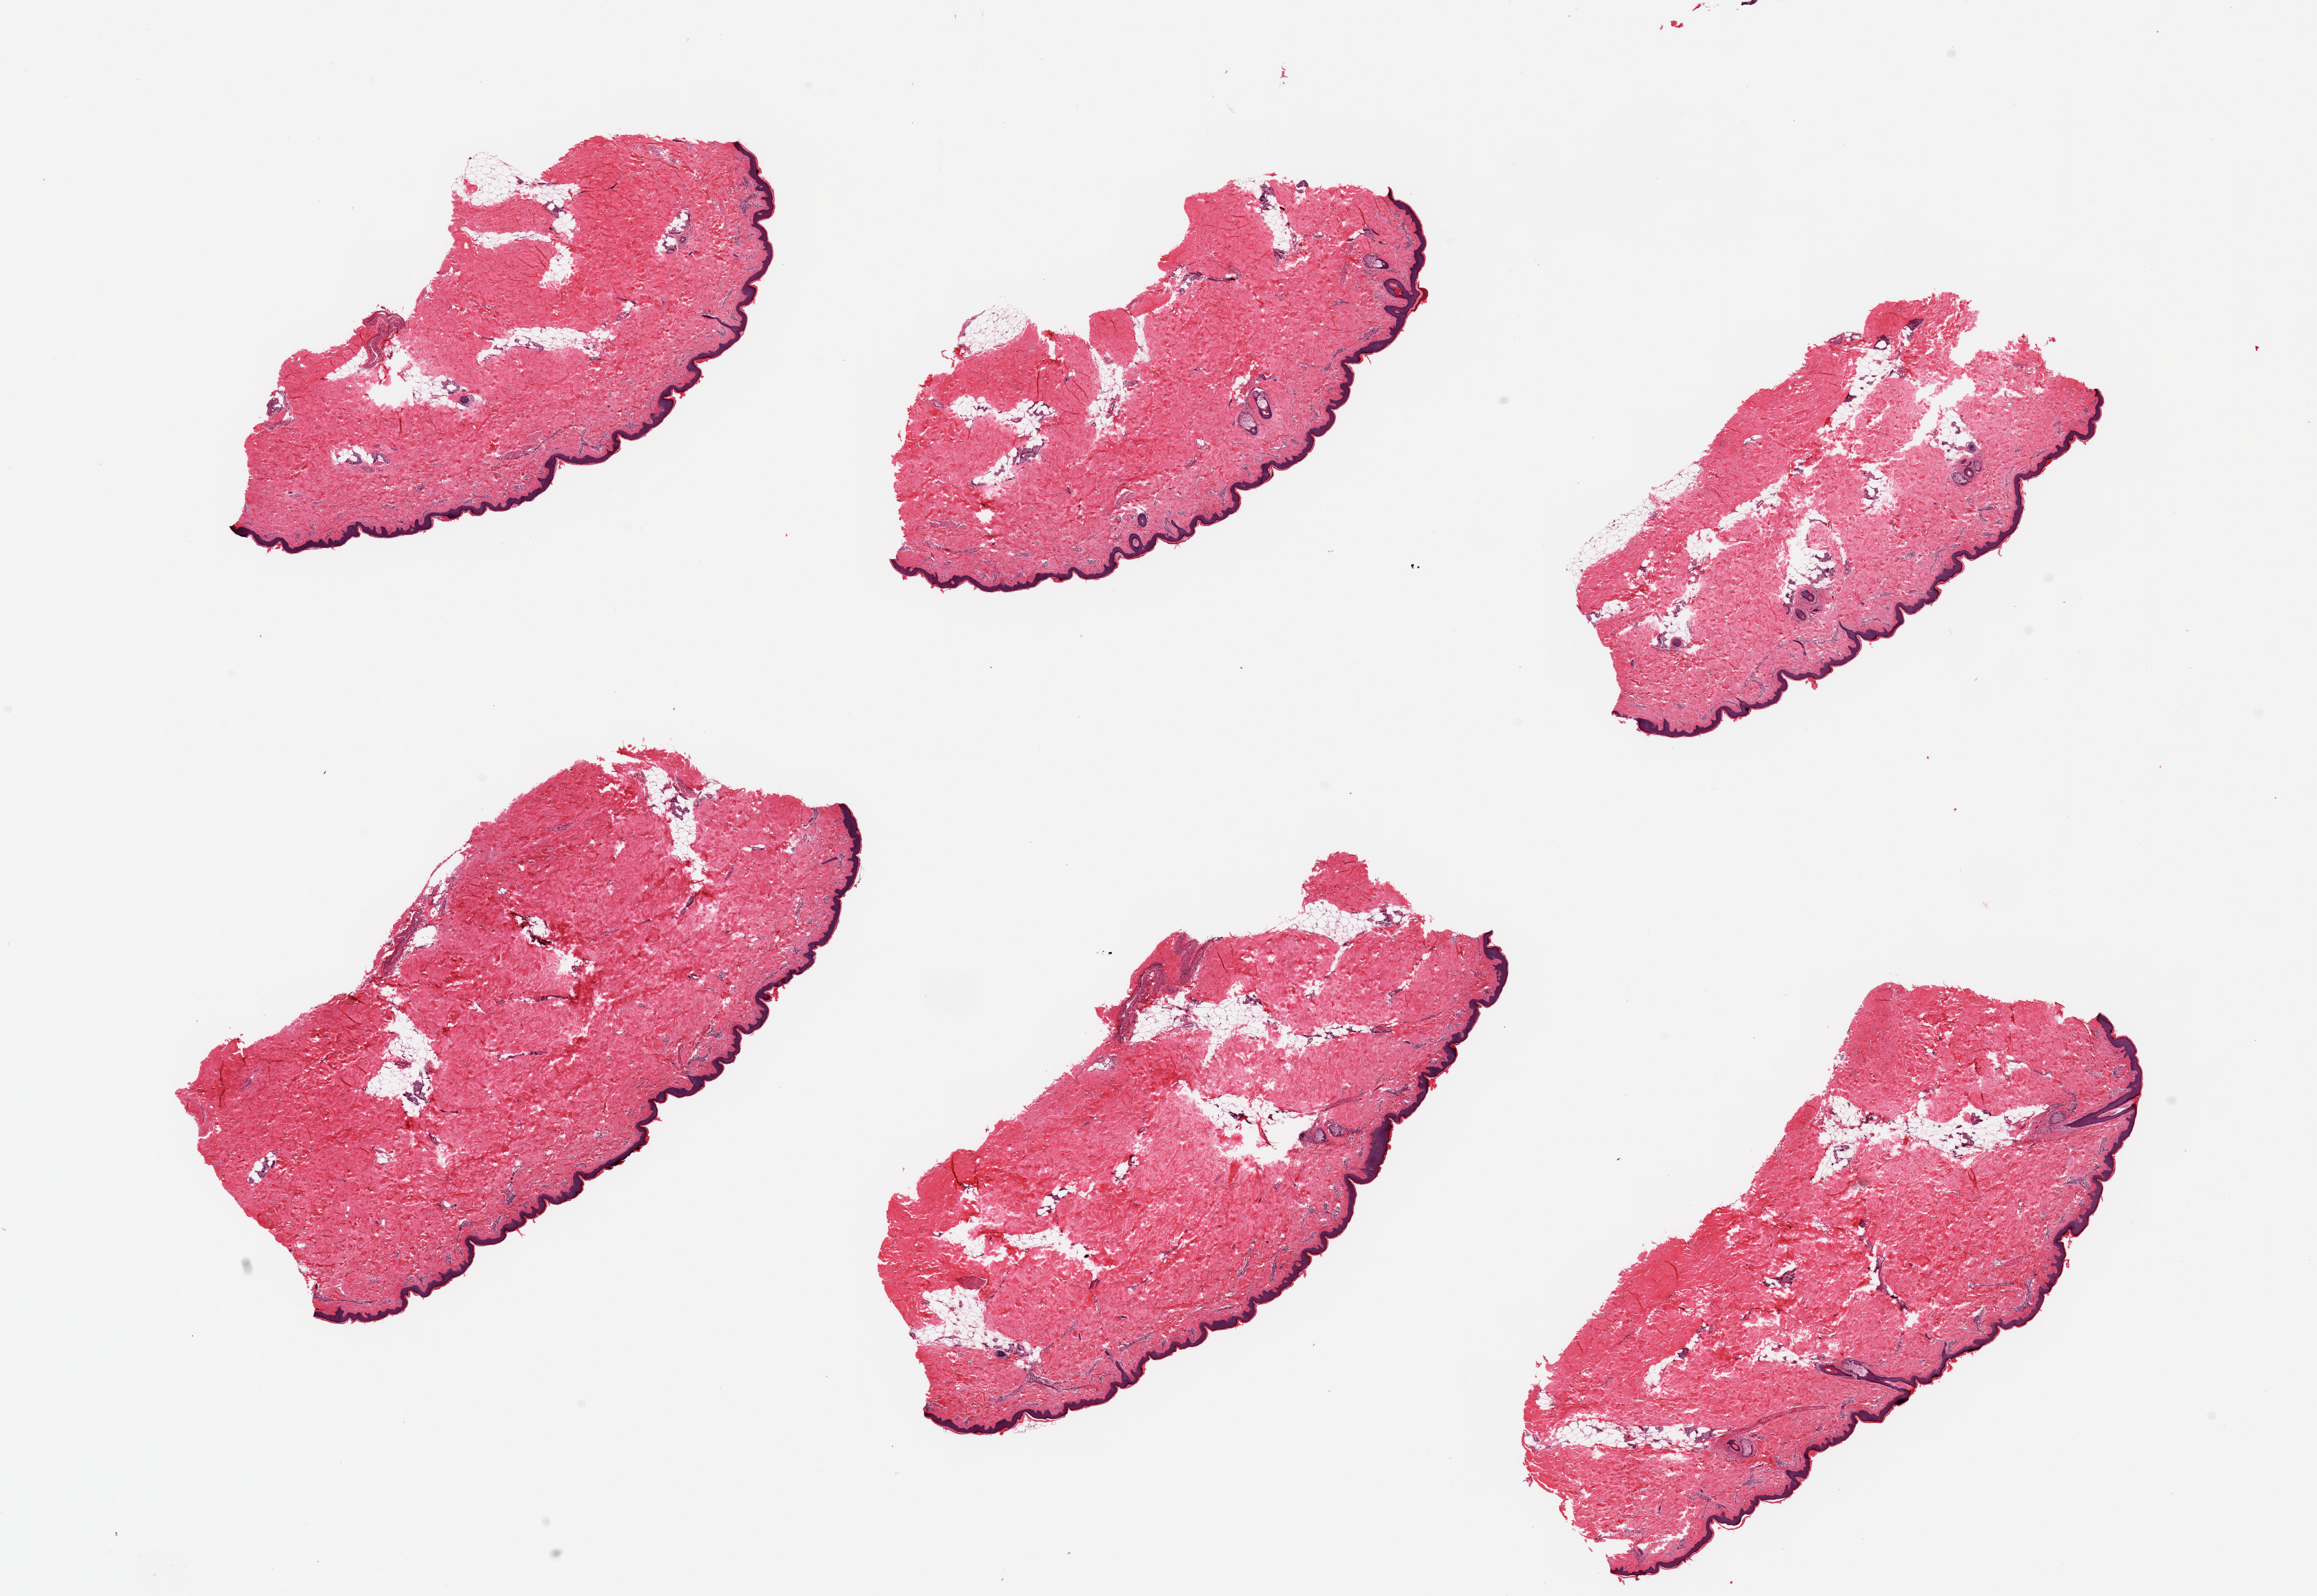
Digitized H&E-stained section — shown as a low-resolution overview of the whole scanned area (about 26.6 x 18.3 mm, slide scanned at 20x). PAXgene-fixed paraffin-embedded (PFPE) section. Target tissue: skin of lower leg. Donor tissue sample.
• reviewer comment on this tissue sample: 6 pieces; ~5-10% internal fat, epidermis measures 57 microns, focal parakeratosis